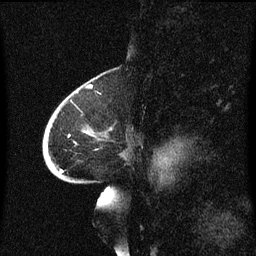
Breast MRI (dynamic contrast-enhanced), one sagittal slice. Position 41 of 60 along the scan axis. Dynamic contrast-enhanced series, image 2 of 3 at this slice position (ordered by acquisition). 1.5 T. TE 4.2 ms, TR 8.4 ms. 2 mm slice thickness. 256 × 256 image matrix, field of view 200 × 200 mm. Female patient, age 68 years. From the clinical record (not read from this slice): setting: breast cancer imaged before/during neoadjuvant chemotherapy; receptor status: triple-negative.
Structures marked on this image (semi-automatically segmented with operator editing):
- analysis volume of interest (the breast-tissue region the enhancement analysis was run in; not a lesion): bounding box [x1, y1, x2, y2] px = [44, 94, 127, 173]
- tumour enhancement mask (voxels above the 70 % enhancement threshold inside the analysis volume of interest): [61, 170, 64, 173]